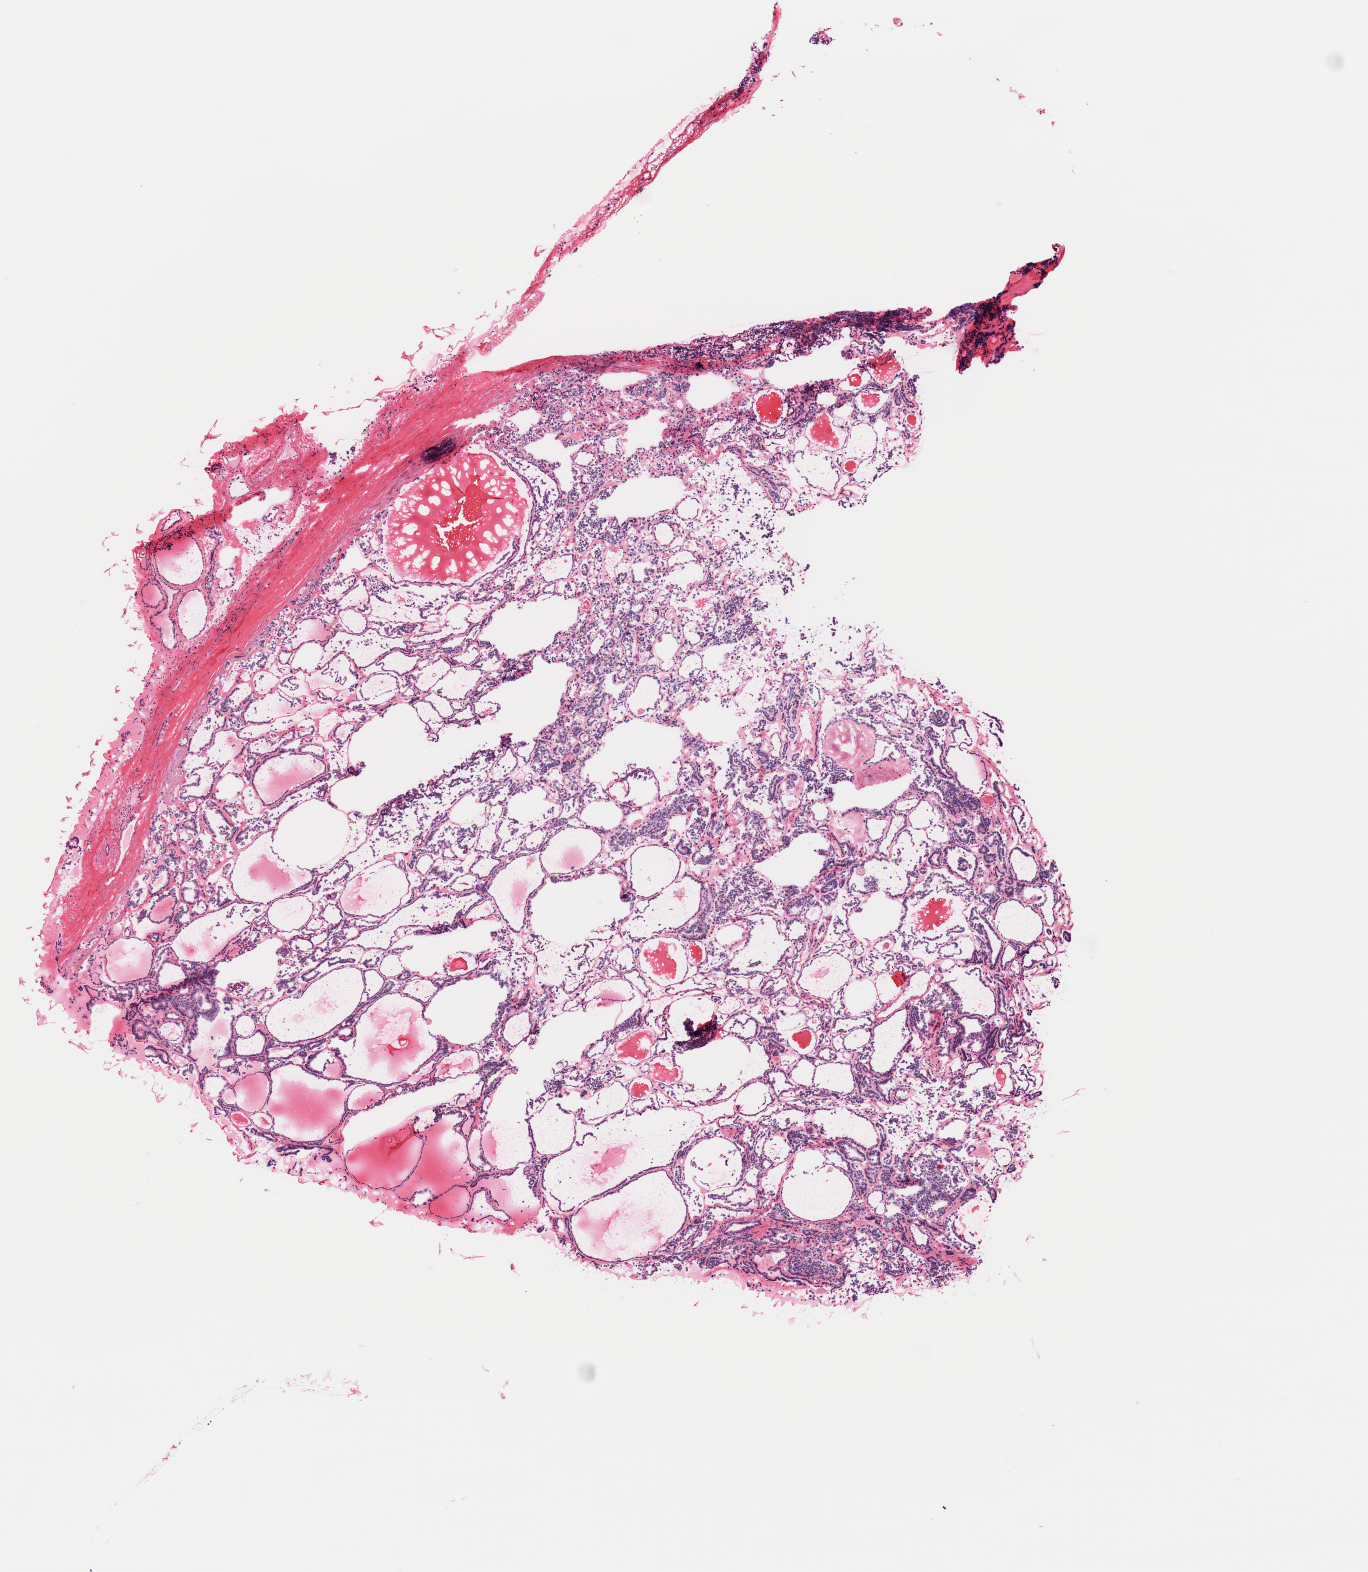
H&E whole-slide image, whole scanned area (about 5.4 x 6.2 mm) shown as a low-resolution overview. Frozen section. Primary tumour sample from the thyroid. Female patient; age at initial diagnosis 51 years. Pathologist review of this section (percent, as recorded): tumour cells 98%, tumour nuclei 98%, normal cells 2%, stromal cells 0%, necrosis 0%. Infiltration values recorded for this section: lymphocyte infiltration 1%, monocyte infiltration 0%, neutrophil infiltration 0%.
• AJCC pathologic stage: III (7th edition)
• lymph nodes positive (case pathology): 4 of 7 examined
• diagnosis: Papillary carcinoma, follicular variant (thyroid gland)